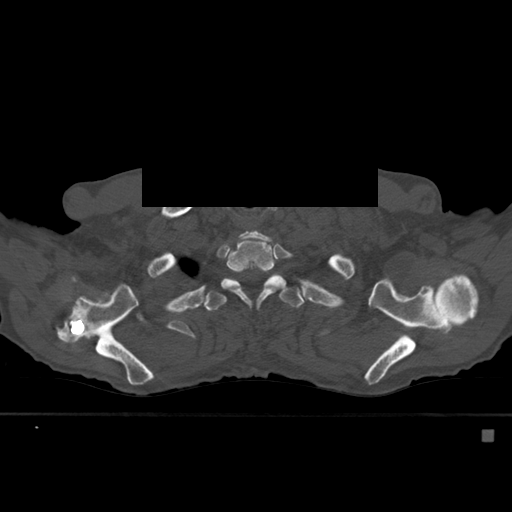
CT including the spine, one axial slice. Slice 442 of 527 in the series (ordered by position). Bone window (W 1800 / L 400 HU). 512 × 512 image matrix, field of view 373 × 373 mm. Male patient, age 78 years. From the clinical record (not read from this slice): primary cancer: prostate.
Structures marked on this image (semi-automatically segmented with operator editing):
- T1 vertebra: bounding box <260,235,269,239> (left, top, right, bottom; pixels)
- T2 vertebra: <226,231,282,304>
- T3 vertebra: <204,269,302,311>